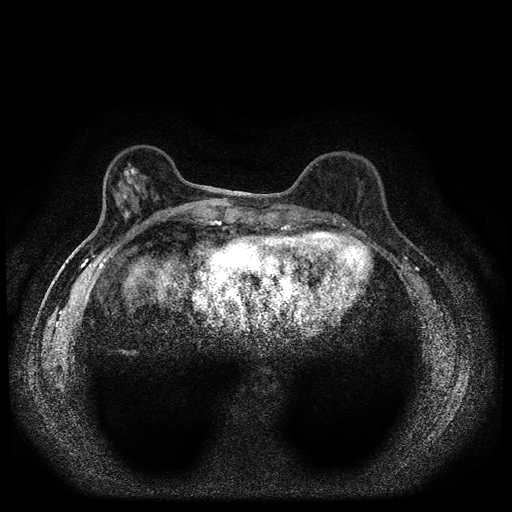
Breast MRI (dynamic contrast-enhanced, multi-phase), one axial slice. Slice 31 of 112 in the series (ordered by position). Dynamic contrast-enhanced series, time point 2 of 5 at this slice position (early post-contrast). 1.5 T. TE 2.7 ms, TR 5.4 ms. 2 mm slice thickness. 512 × 512 image matrix, field of view 320 × 320 mm. Female patient, age 61 years.
Annotated regions visible in this slice (semi-automatically segmented with operator editing):
- breast lesion (labelled benign in the annotation): box from (x=117, y=162) to (x=146, y=219) px